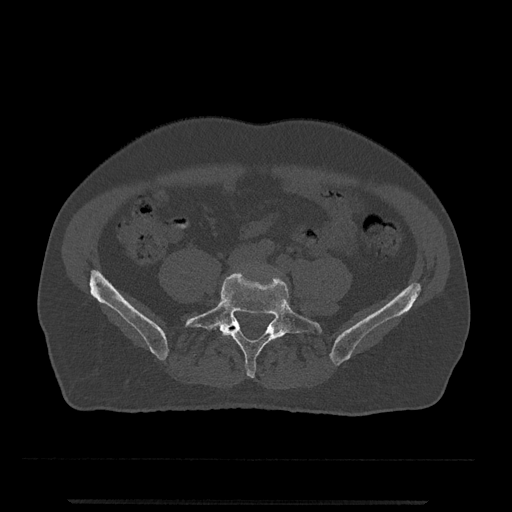
CT including the spine, one axial slice. Position 80 of 797 along the scan axis. Bone window (W 1800 / L 400 HU). 0.5 mm slice thickness. 512 × 512 image matrix. Patient: male, 63 years. Case-level facts recorded for this patient, not image findings: primary cancer: prostate.
Structures marked on this image (semi-automatically segmented with operator editing):
- L4 vertebra: box from (x=229, y=321) to (x=235, y=327) px
- L5 vertebra: (x=184, y=273)–(x=323, y=378)